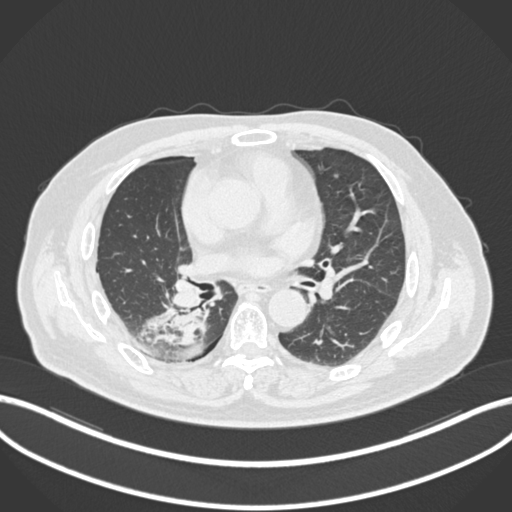
Chest CT, one axial slice; slice 96 of 218 in the series (ordered by position); reconstruction kernel B30f; lung window (W 1500 / L -600 HU); 1 mm slice thickness; 512 × 512 image matrix. Male patient, age 68 years. From the clinical record (not read from this slice): clinical TNM (as recorded): T2a N0 M0.
Annotated regions visible in this slice (rectangle marked by the reading radiologist):
- lung tumour (recorded histology: adenocarcinoma): box from (x=135, y=298) to (x=208, y=361) px